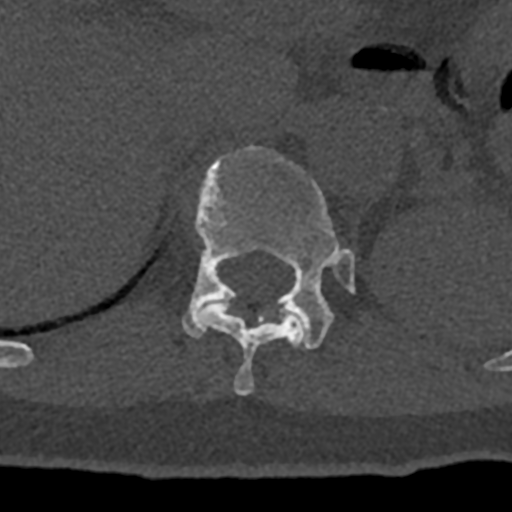
CT including the spine, one axial slice. Slice 516 of 797 in the series (ordered by position). Reconstruction kernel Br40s/3. 120 kVp. Bone window (W 1800 / L 400 HU). 512 × 512 image matrix, field of view 160 × 160 mm. Patient: male, 74 years. From the clinical record (not read from this slice): primary cancer: renal.
Structures marked on this image (semi-automatic segmentation, software-assisted and operator-edited):
- T11 vertebra: bounding box [x1, y1, x2, y2] px = [196, 302, 305, 396]
- T12 vertebra: [182, 145, 355, 349]